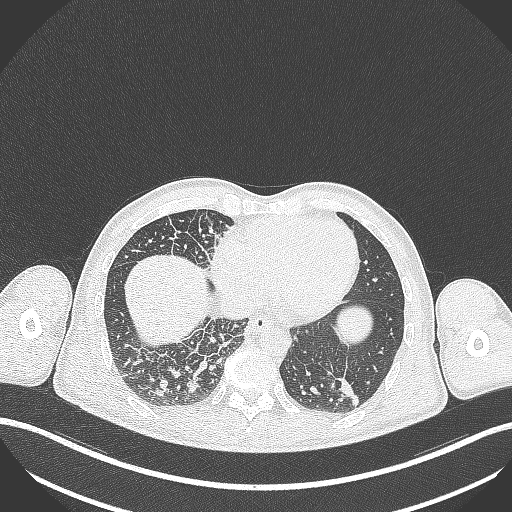
Chest CT, one axial slice; slice 86 of 348 in the series (ordered by position); lung window (W 1500 / L -600 HU); 1 mm slice thickness; 512 × 512 image matrix. Patient: male, 49 years. Case-level facts recorded for this patient, not image findings: clinical TNM (as recorded): T2b N1 M0.
Outlined on this slice (bounding box drawn by a radiologist):
- lung tumour (recorded histology: adenocarcinoma): bounding box (x1, y1, x2, y2) in pixels: (335, 372, 361, 407)